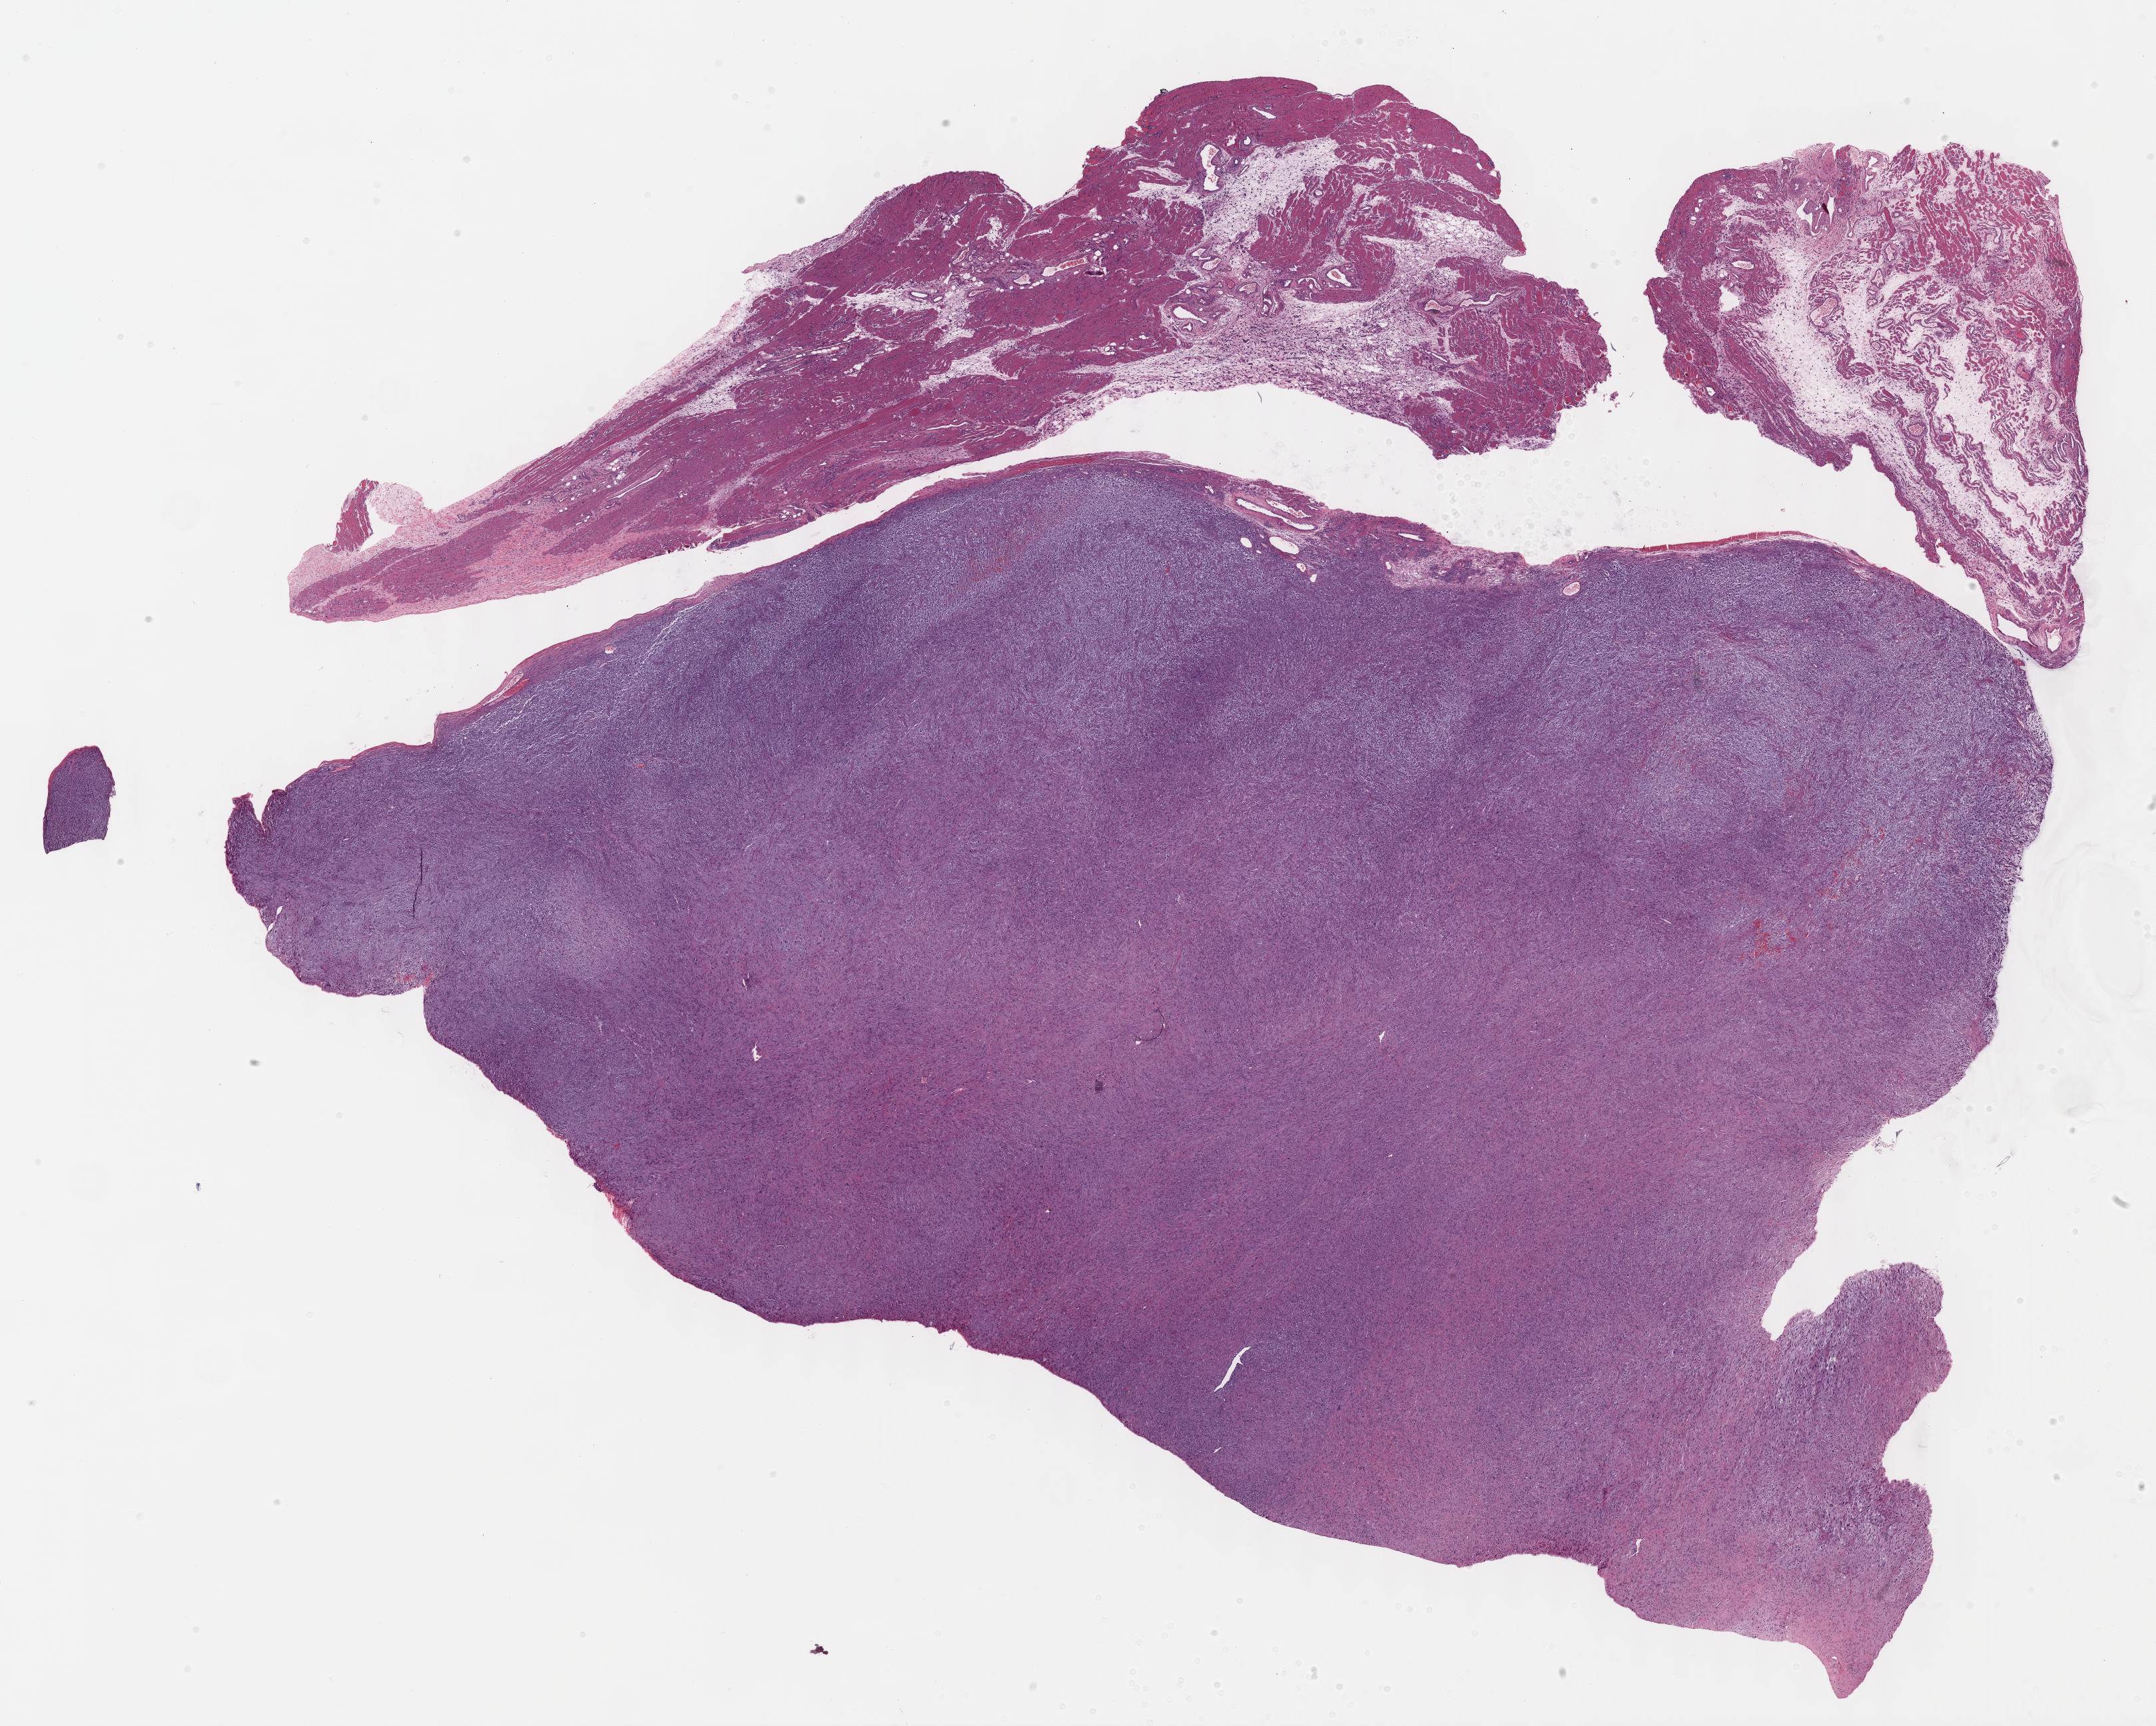
Digitized Hematoxylin and eosin (H&E) stained tissue section (whole slide), shown as a low-resolution overview of the whole scanned area (about 26.2 x 20.9 mm, slide scanned at 40x); formalin-fixed paraffin-embedded (FFPE) diagnostic section; sample: primary tumour, connective, subcutaneous and other soft tissues. Patient sex: female.
Histologic diagnosis: Undifferentiated sarcoma (connective, subcutaneous and other soft tissues of lower limb and hip).